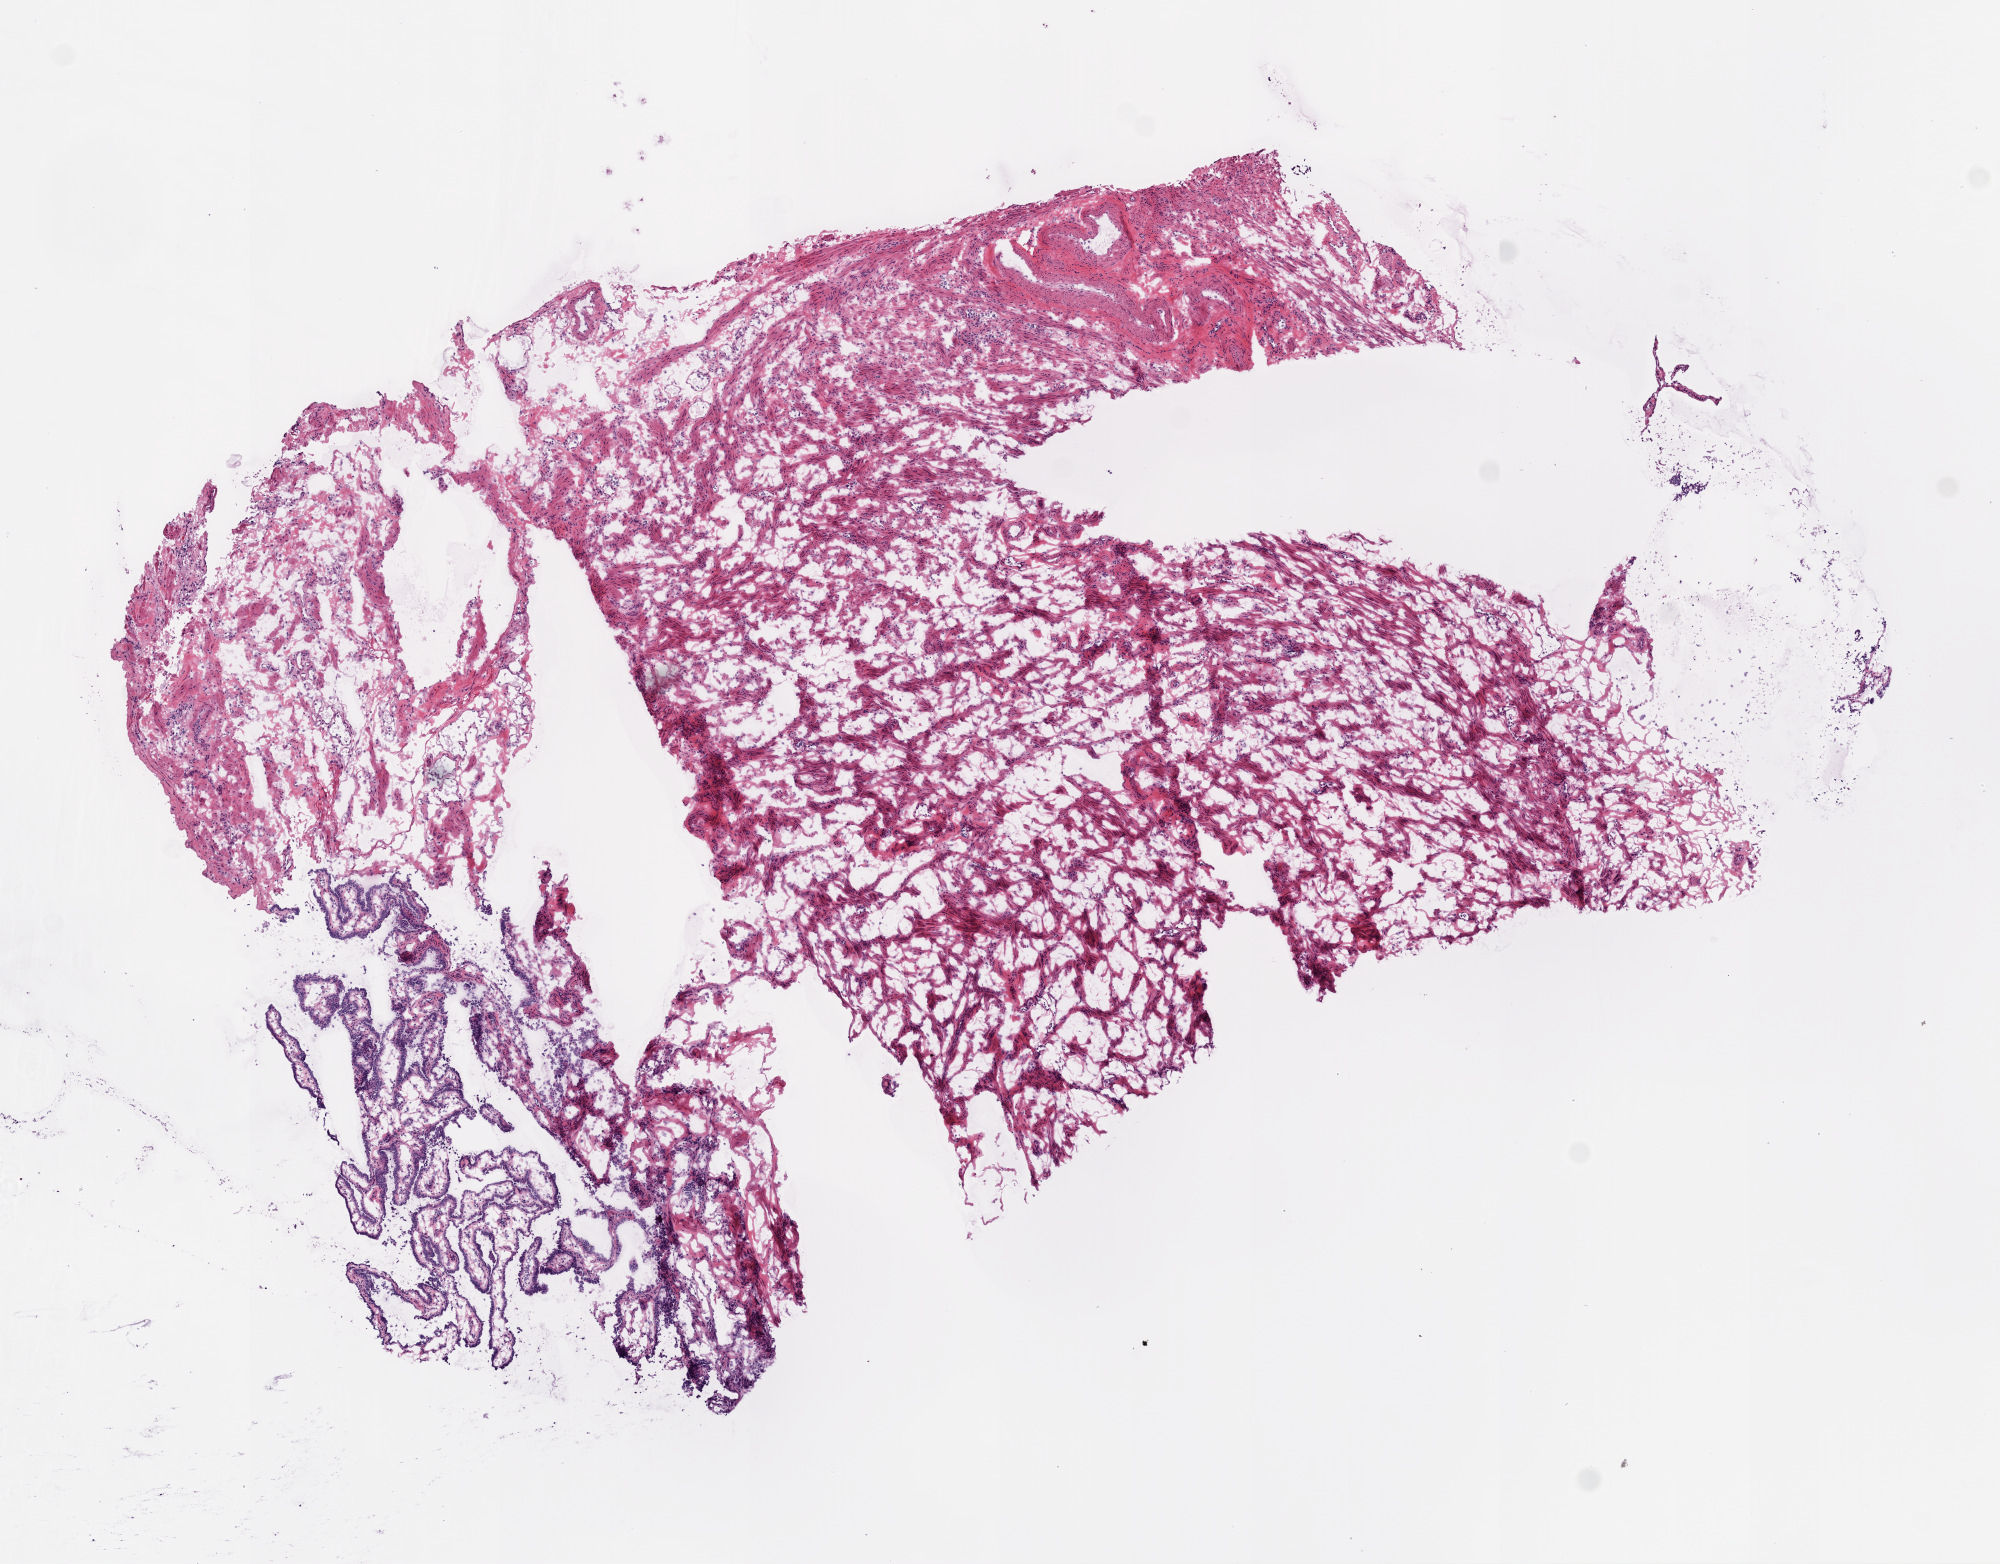
H&E-stained whole-slide image — low-resolution overview of the scanned area, about 8.0 x 6.3 mm (slide scanned at 20x), frozen section from the bottom of the tissue portion, ovary, solid tissue normal (non-tumour tissue) sample. Female patient; age at initial diagnosis 54 years.
This section: solid tissue normal (non-tumour) sample from the same patient. Patient diagnosis: Serous cystadenocarcinoma, NOS.